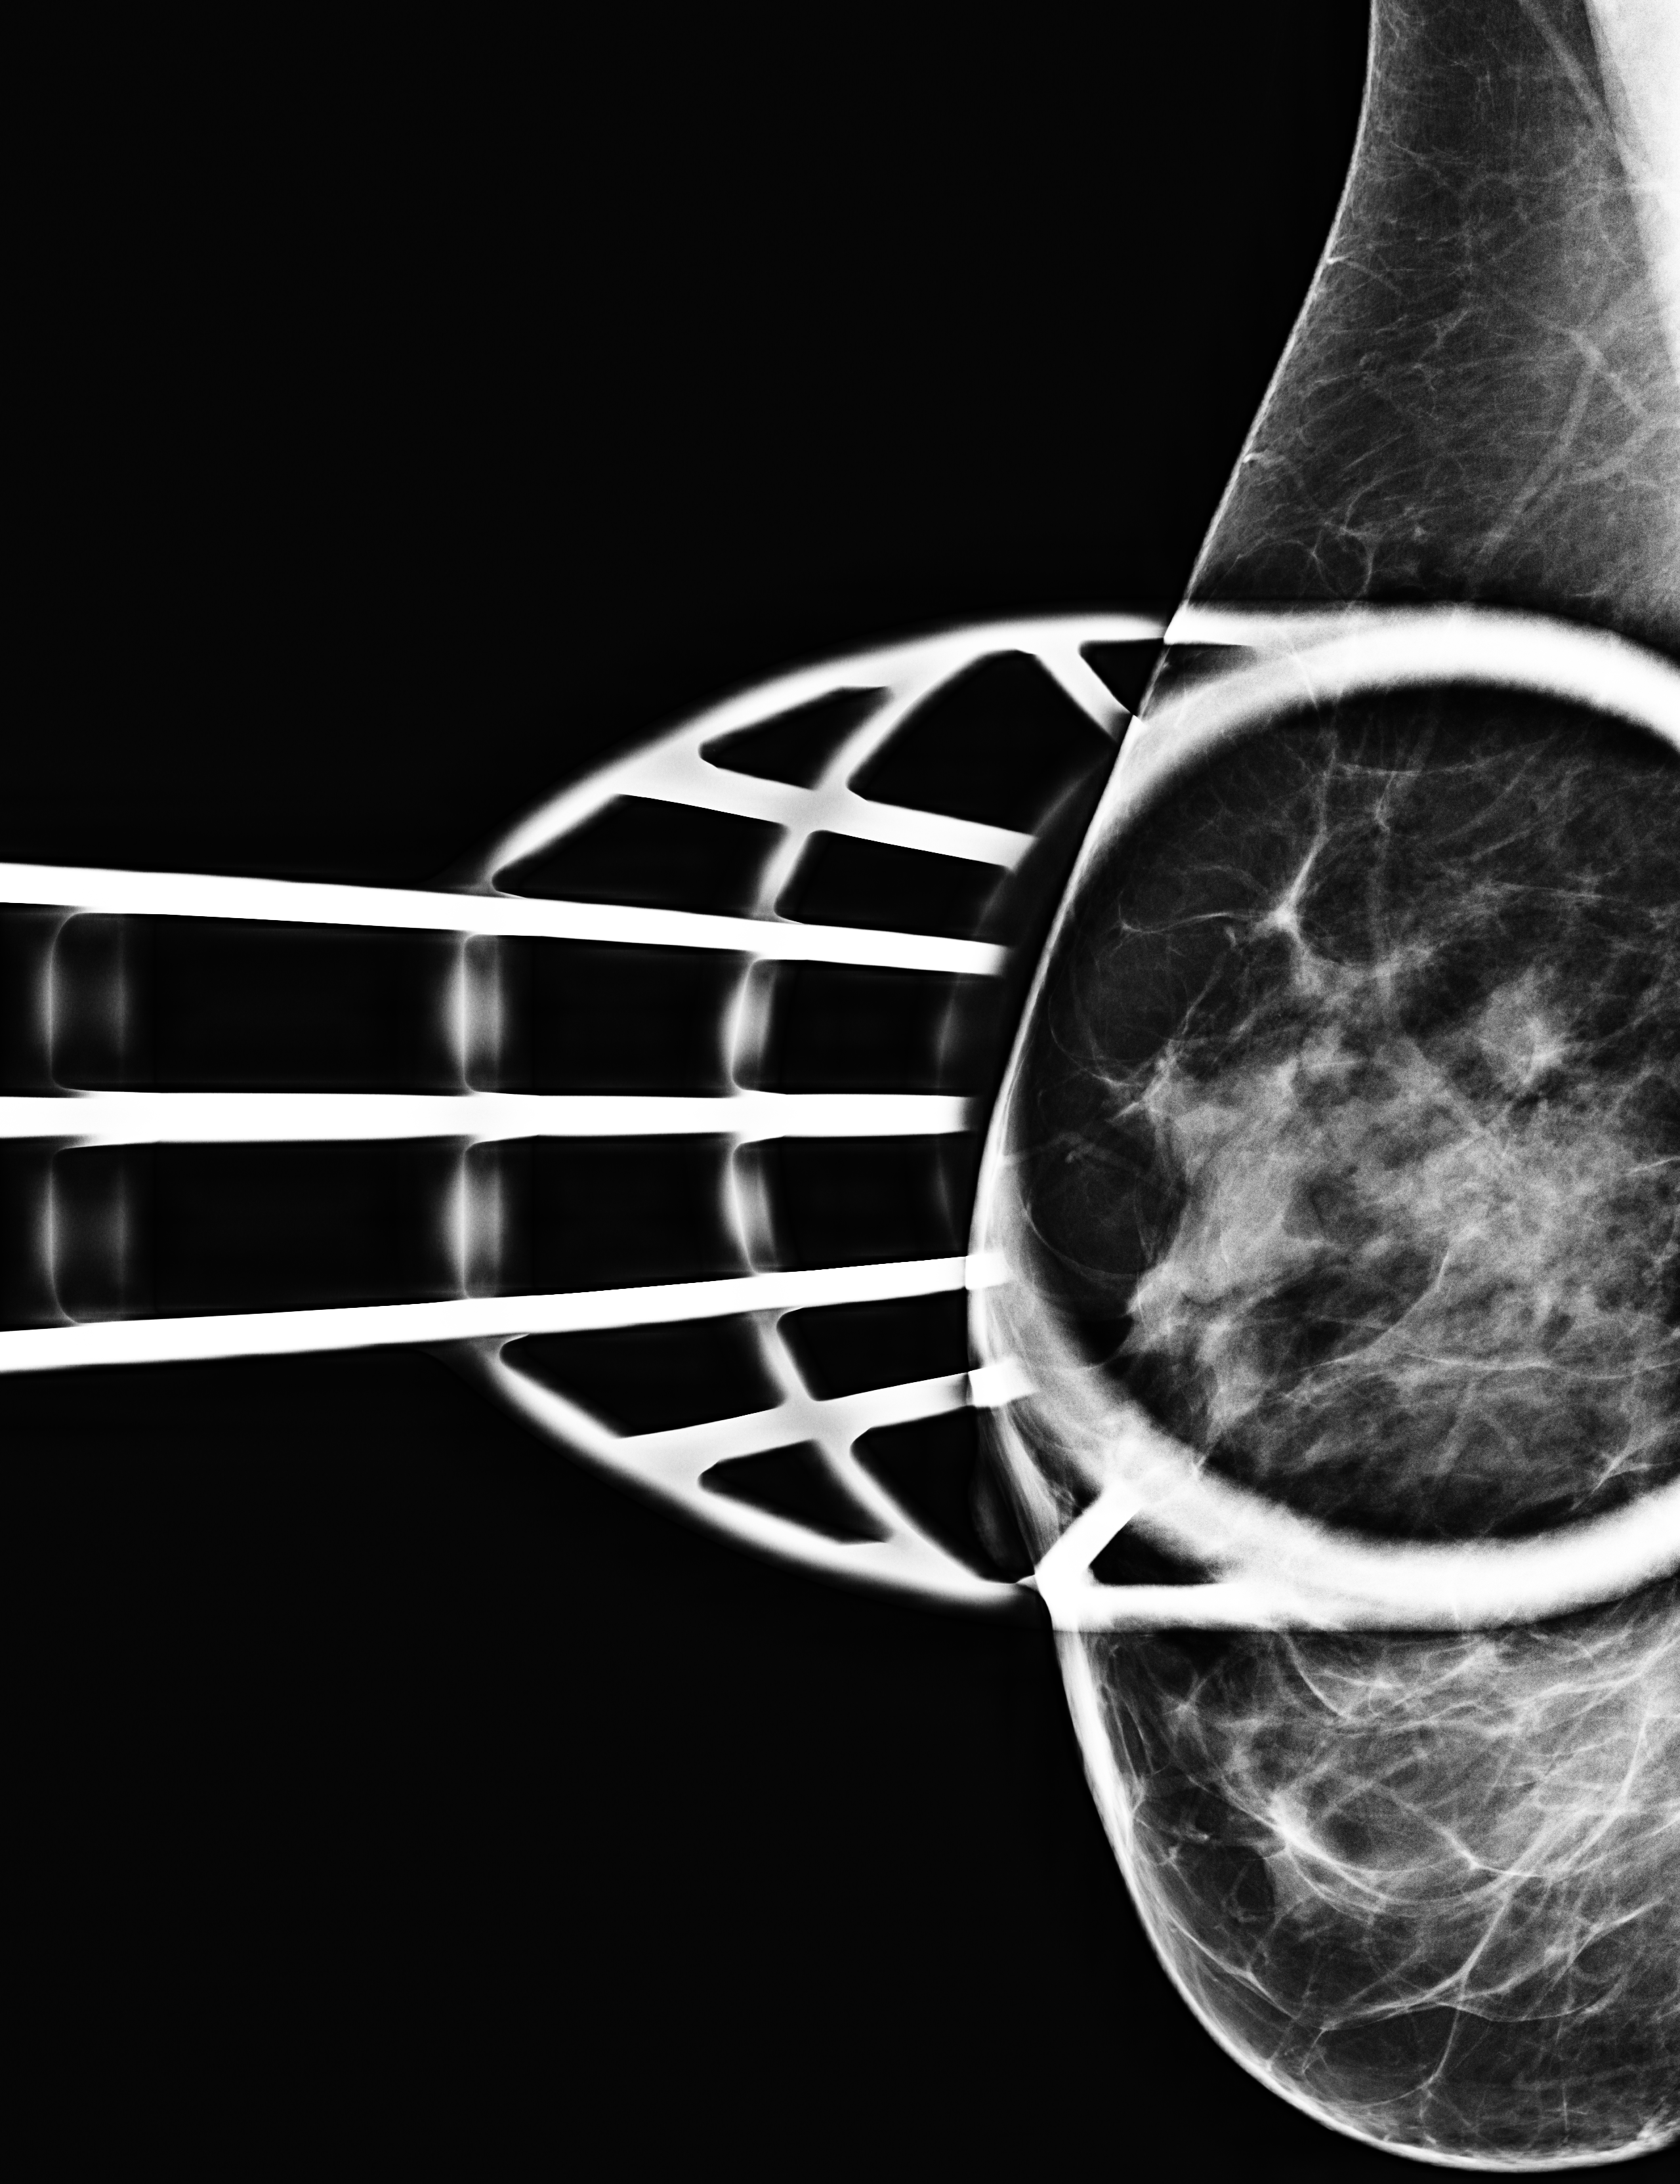
Additional work-up view, compressed breast thickness 47 mm. Female patient, age 43 years.
Image type: full-field digital mammogram. Breast: right. Projection: medio-lateral oblique projection, spot compression.